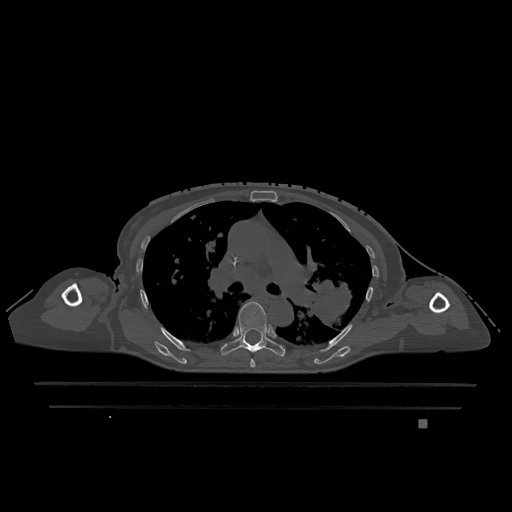
CT including the spine, one axial slice. Slice 798 of 1317 in the series (ordered by position). Bone window (W 1800 / L 400 HU). 0.5 mm slice thickness. 512 × 512 image matrix, field of view 500 × 500 mm. Patient: female, 74 years. Case-level facts recorded for this patient, not image findings: primary cancer: lung; vertebrae with lytic lesions (as recorded): T1, T4, T5, T6, L4, L5.
Structures marked on this image (semi-automatic segmentation, software-assisted and operator-edited):
- T5 vertebra: box from (x=250, y=359) to (x=255, y=368) px
- T6 vertebra: (x=221, y=301)–(x=285, y=357)